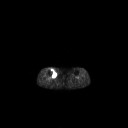
FDG PET of an extremity soft-tissue mass (from a PET/CT study), one axial slice; position 144 of 267 along the scan axis; 3.27 mm slice thickness; 128 × 128 image matrix. Patient: female, 65 years. From the clinical record (not read from this slice): histological type: undifferentiated – high grade; grade: high; site of the primary tumour: right thigh.
Outlined on this slice (expert contour drawn on MRI and transferred to this co-registered scan by the dataset authors):
- gross tumour volume (mass): bounding box (x1, y1, x2, y2) in pixels: (50, 68, 57, 77)